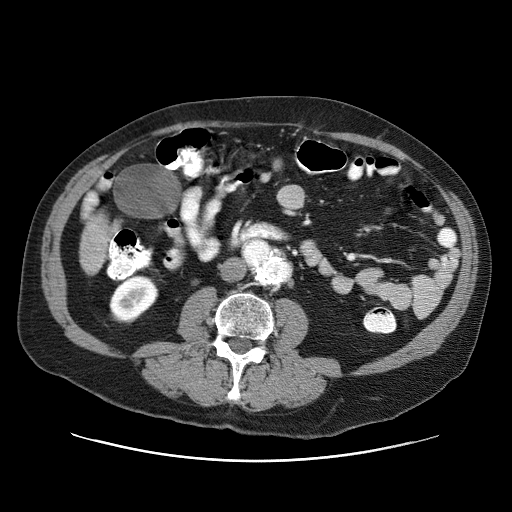
Contrast-enhanced abdominal CT (liver protocol), one axial slice; slice 3 of 87 in the series (ordered by position); 120 kVp; one of 3 acquisitions stored at this slice position; soft-tissue window (W 400 / L 40 HU); 2.5 mm slice thickness; 512 × 512 image matrix, field of view 400 × 400 mm. From the clinical record (not read from this slice): diagnosis: hepatocellular carcinoma (patient treated with transarterial chemoembolisation; whether this scan precedes or follows treatment is not stated here); TNM stage (as recorded): Stage-IIIA; Child-Pugh class: A; tumour nodularity: multinodular; tumour size: 6 cm.
Annotated regions visible in this slice (semi-automatically segmented with operator editing):
- liver parenchyma outside the tumour (the mass and vessels are separate outlines, so this box may not span the whole liver): box from (x=80, y=192) to (x=110, y=274) px
- liver vessels: (x=88, y=195)–(x=95, y=202)